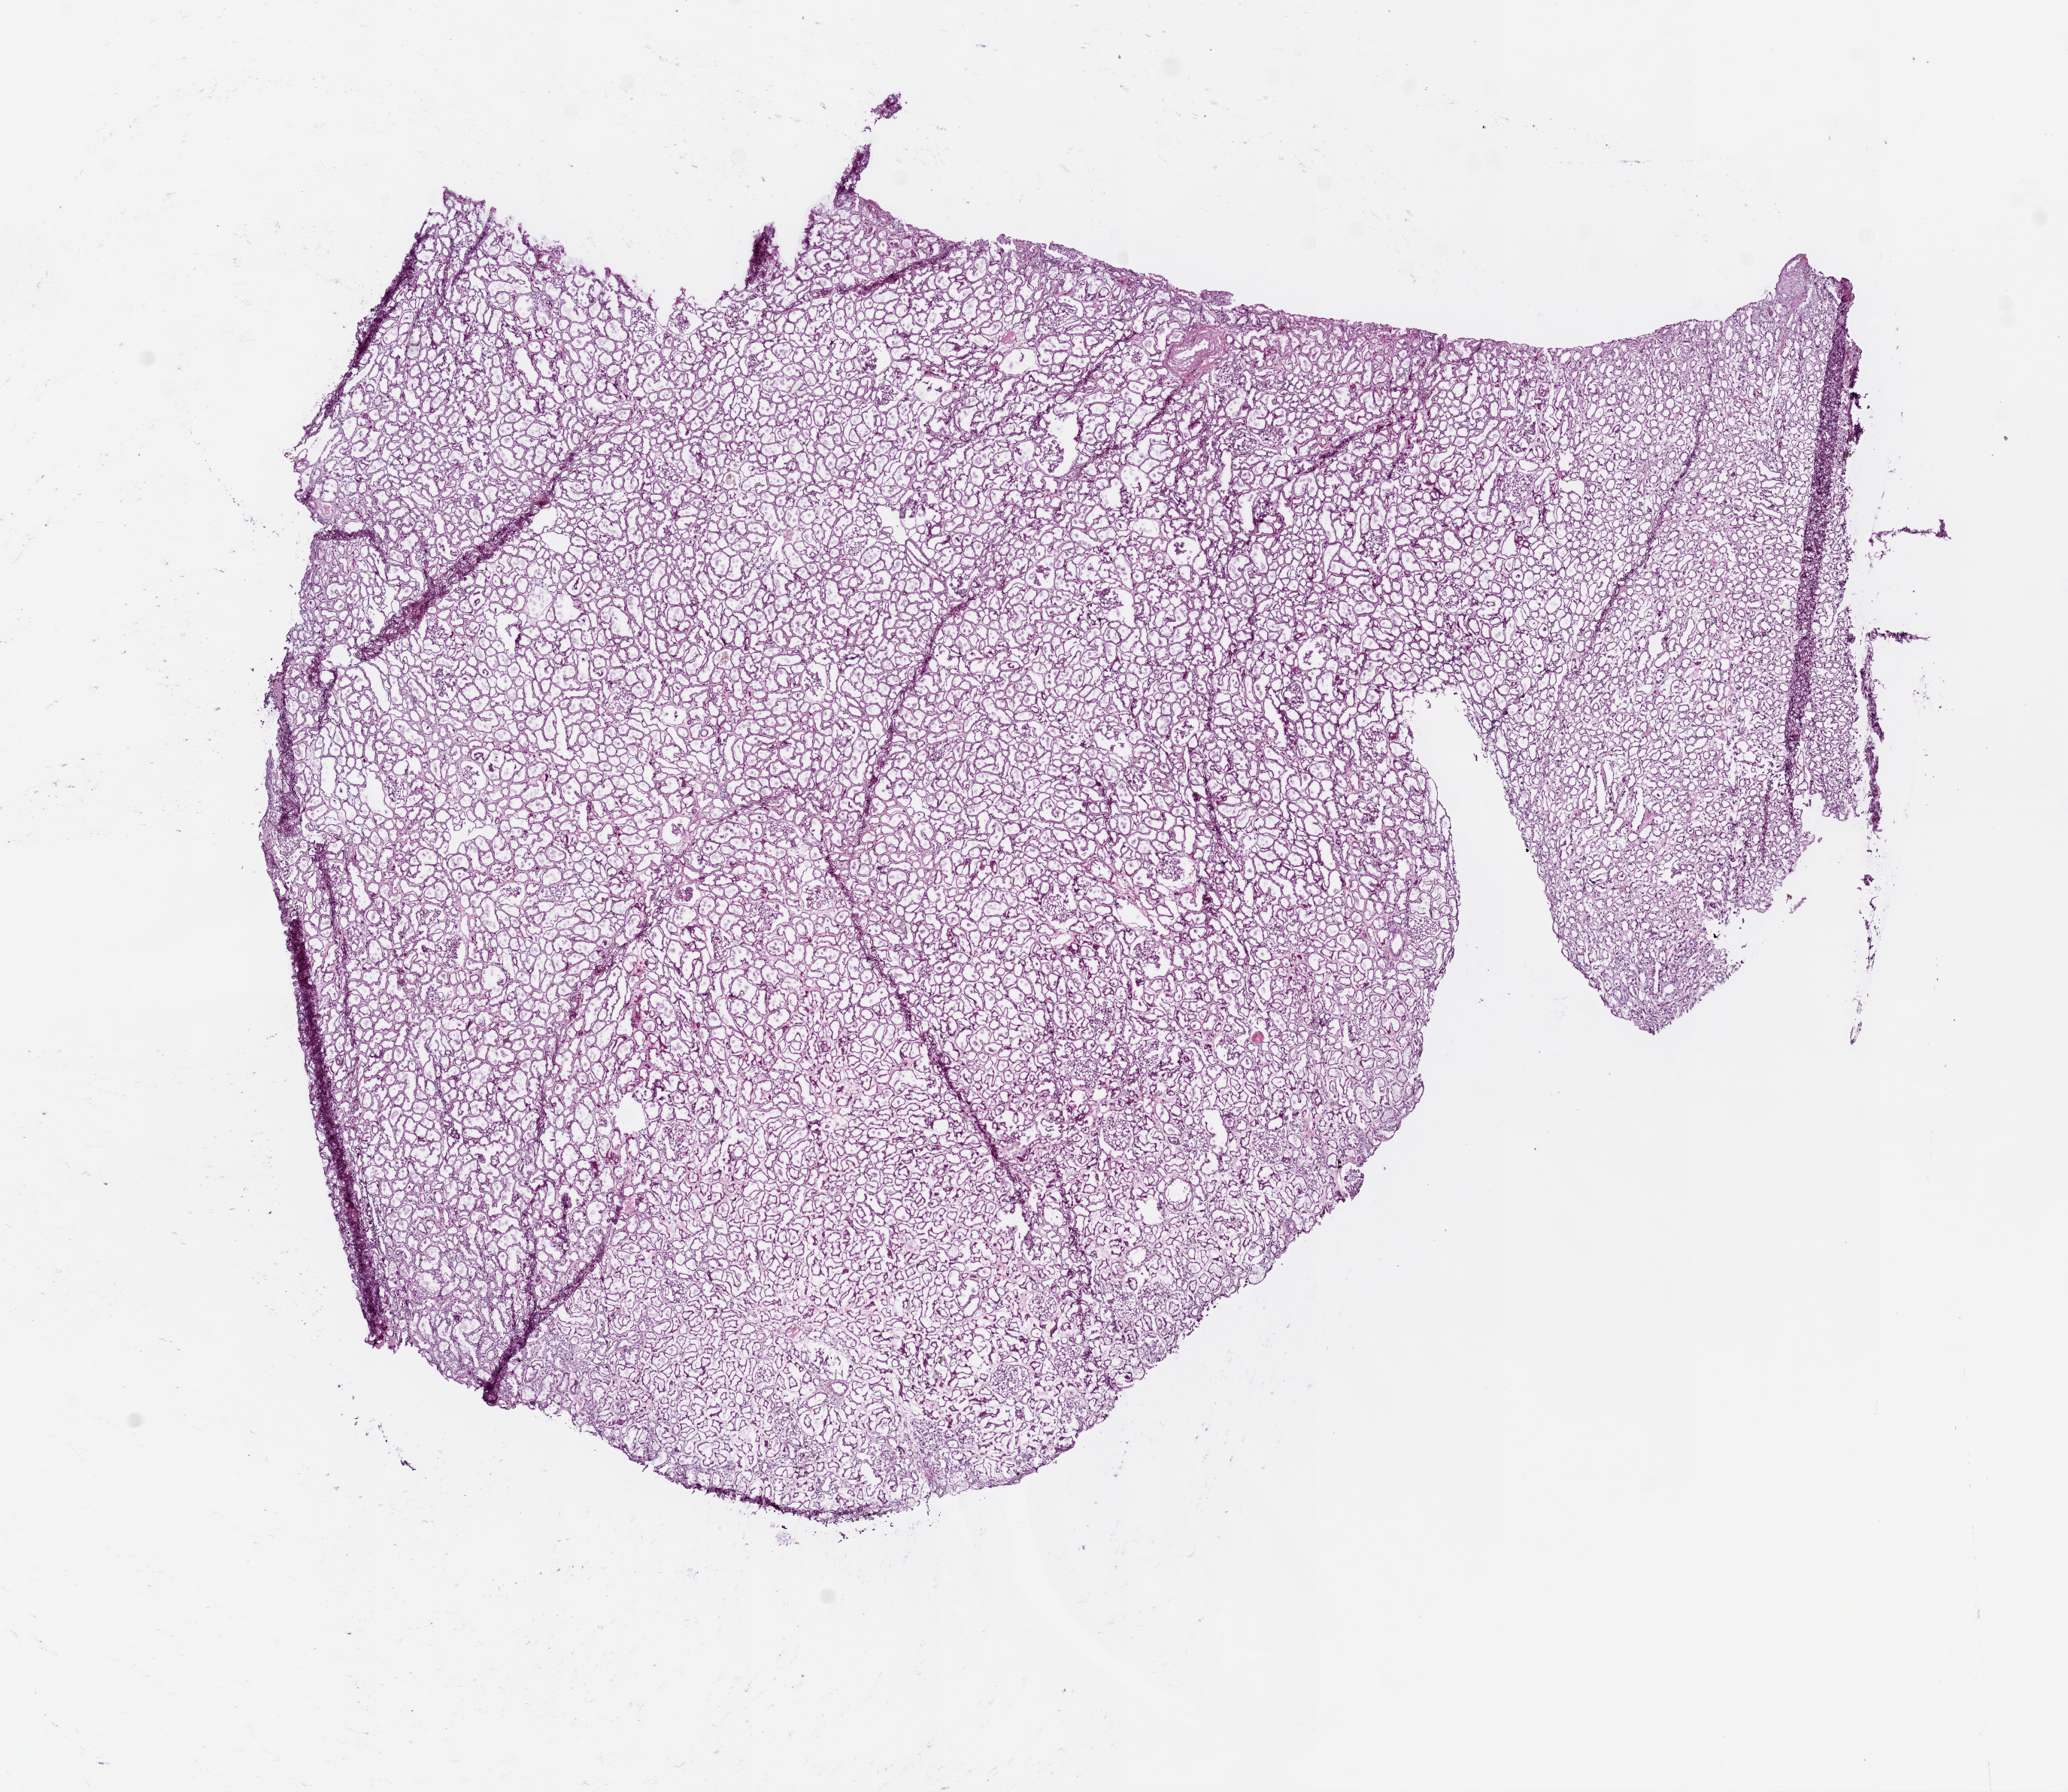
Hematoxylin and eosin (H&E) stained whole-slide image — low-resolution overview of the scanned area, about 11.0 x 9.6 mm (slide scanned at 20x); frozen section from the bottom of the tissue portion; solid tissue normal (non-tumour tissue) sample from the kidney. Male, age 61 years at initial diagnosis.
* this section: solid tissue normal sample (biorepository sample class)
* patient diagnosis: Clear cell adenocarcinoma, NOS